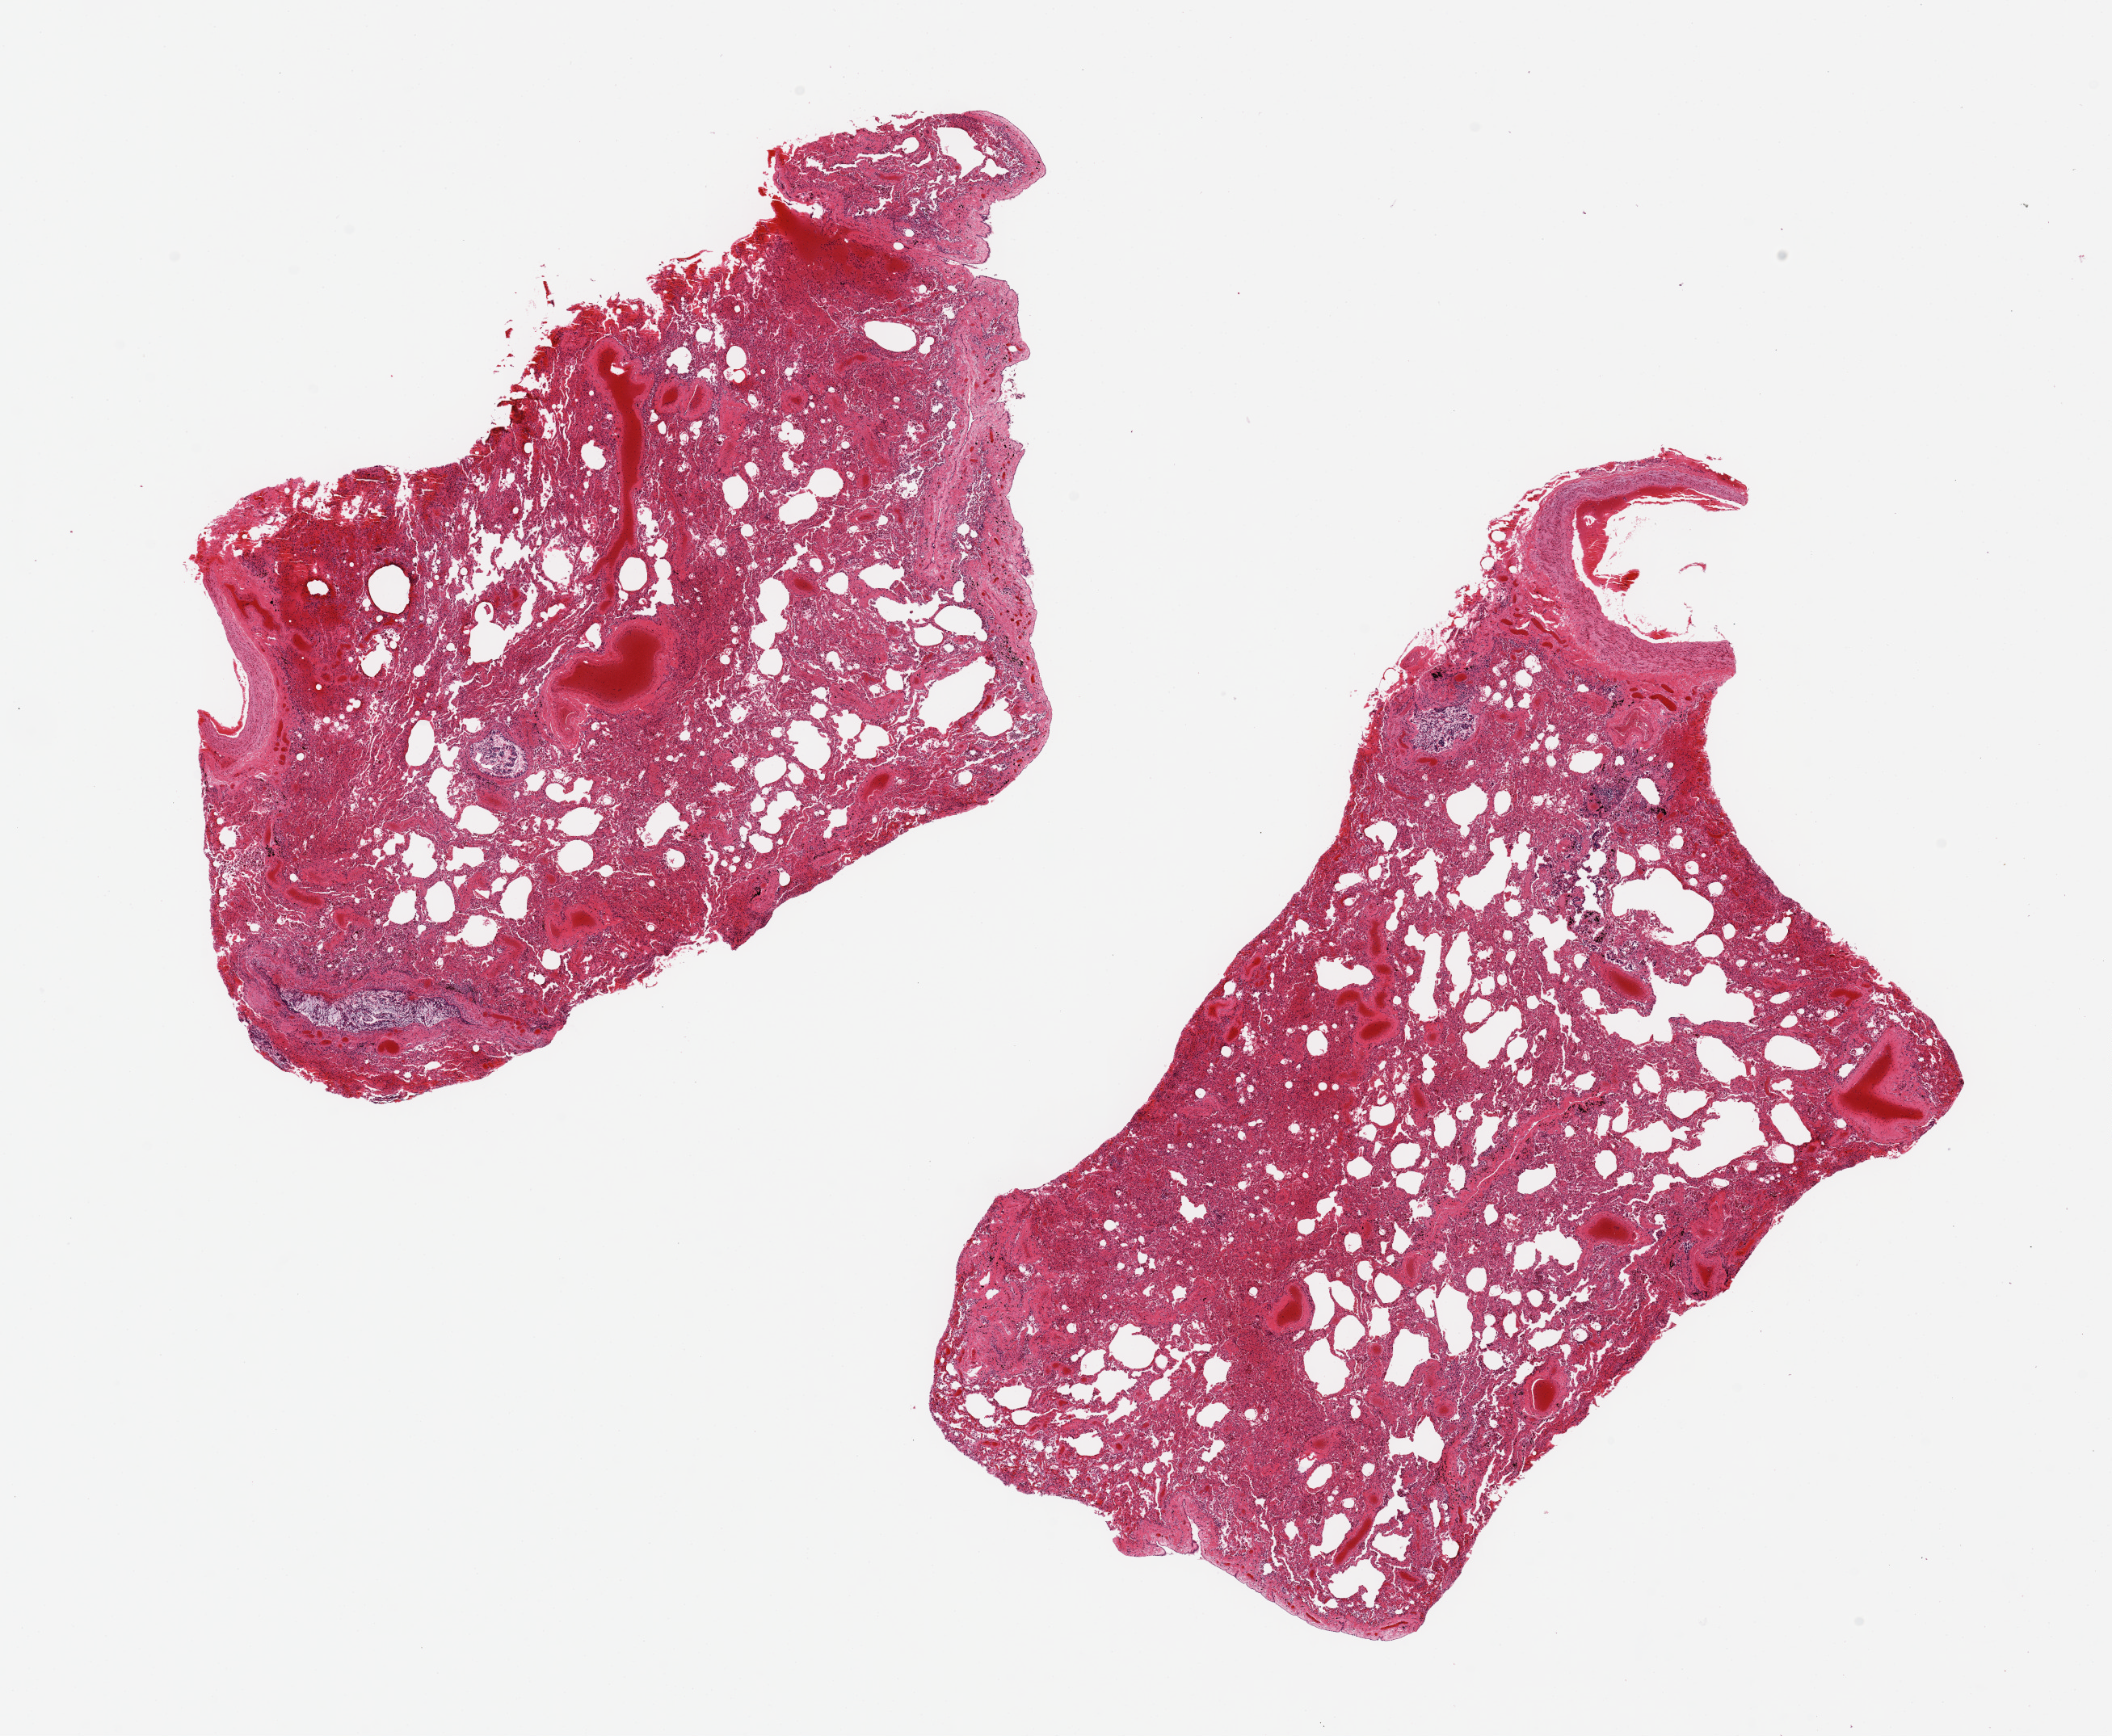
Digitized hematoxylin and eosin (H&E)-stained section, brightfield, shown as a low-resolution overview of the whole scanned area (about 20.7 x 17.0 mm, from a 20x scan); PAXgene-fixed paraffin-embedded (PFPE) section; sampled site (target tissue): lung; donor tissue sample. Donor sex: male.
• pathologist's review note for this sample: 2 aliquots, ~8x6mm. Probable diffuse congestion, too autolyzed for definitive assessment